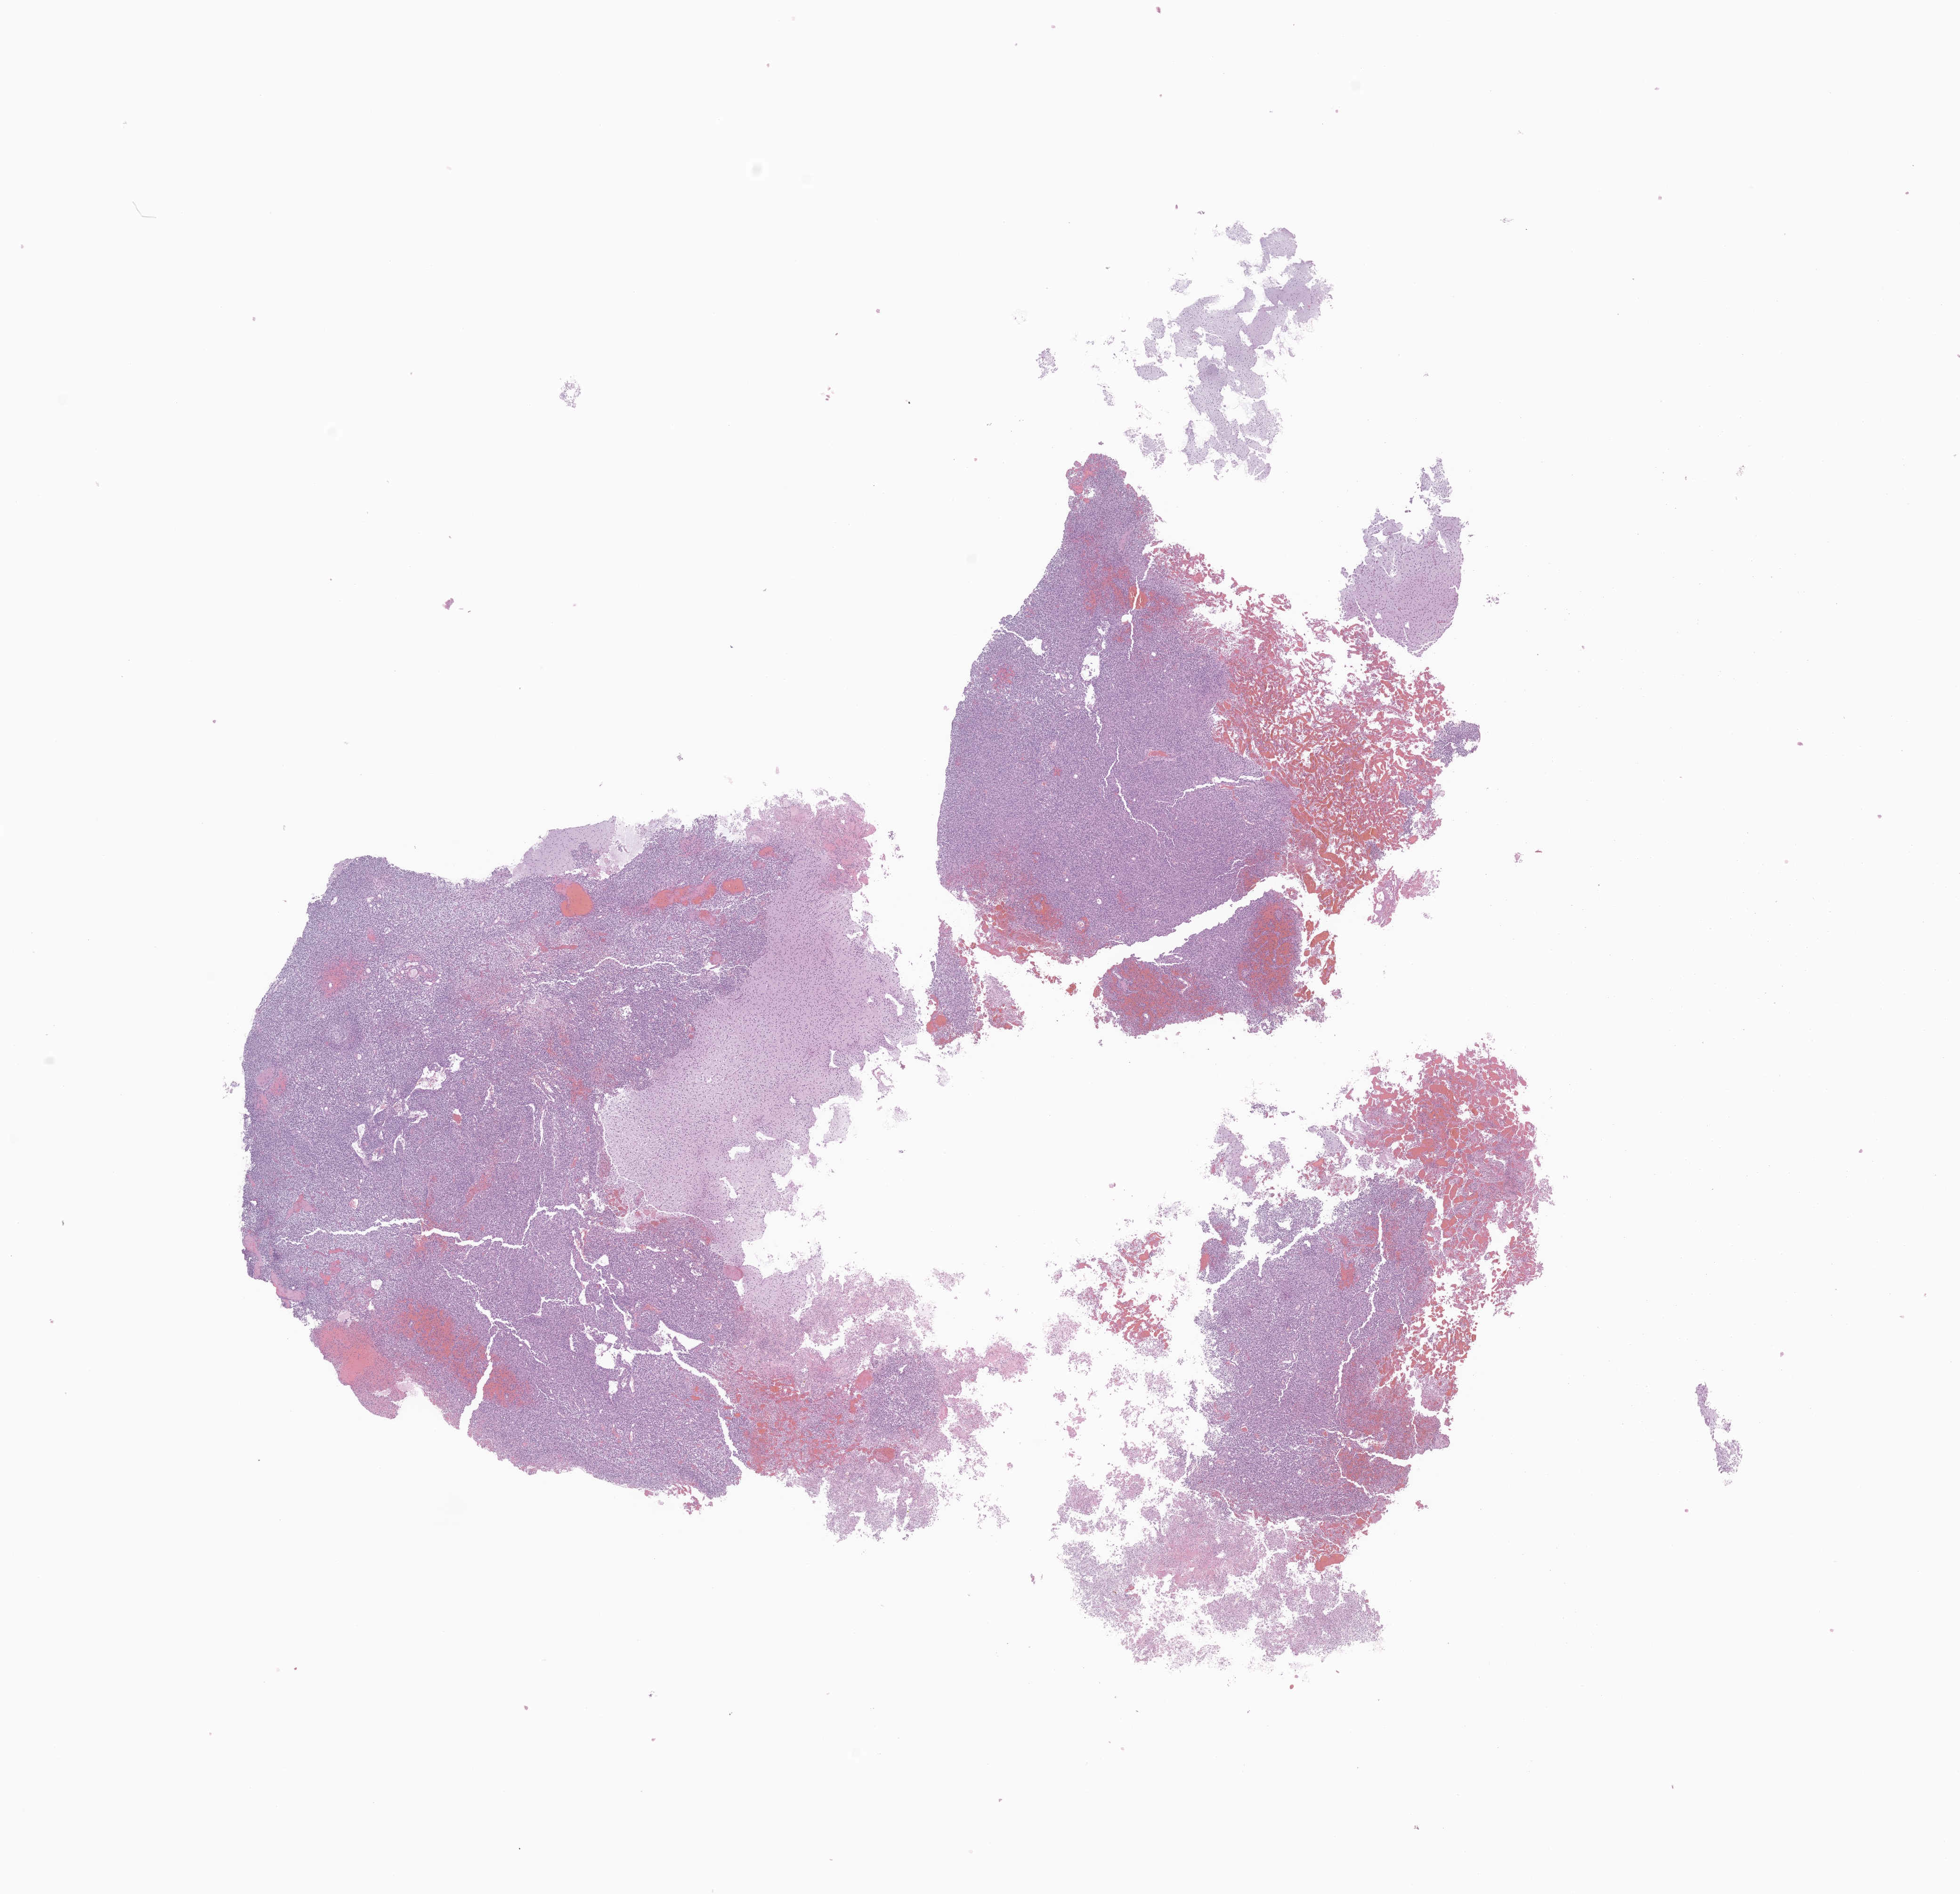
Haematoxylin and eosin whole-slide image of tumor tissue from the temporal lobe, shown as a low-resolution overview of the whole scanned area (about 17.5 x 17.0 mm), formalin-fixed, paraffin-embedded (FFPE) tissue. Patient female; age 29 days.
- diagnosis (ICD-O-3 morphology term): Glioma, malignant